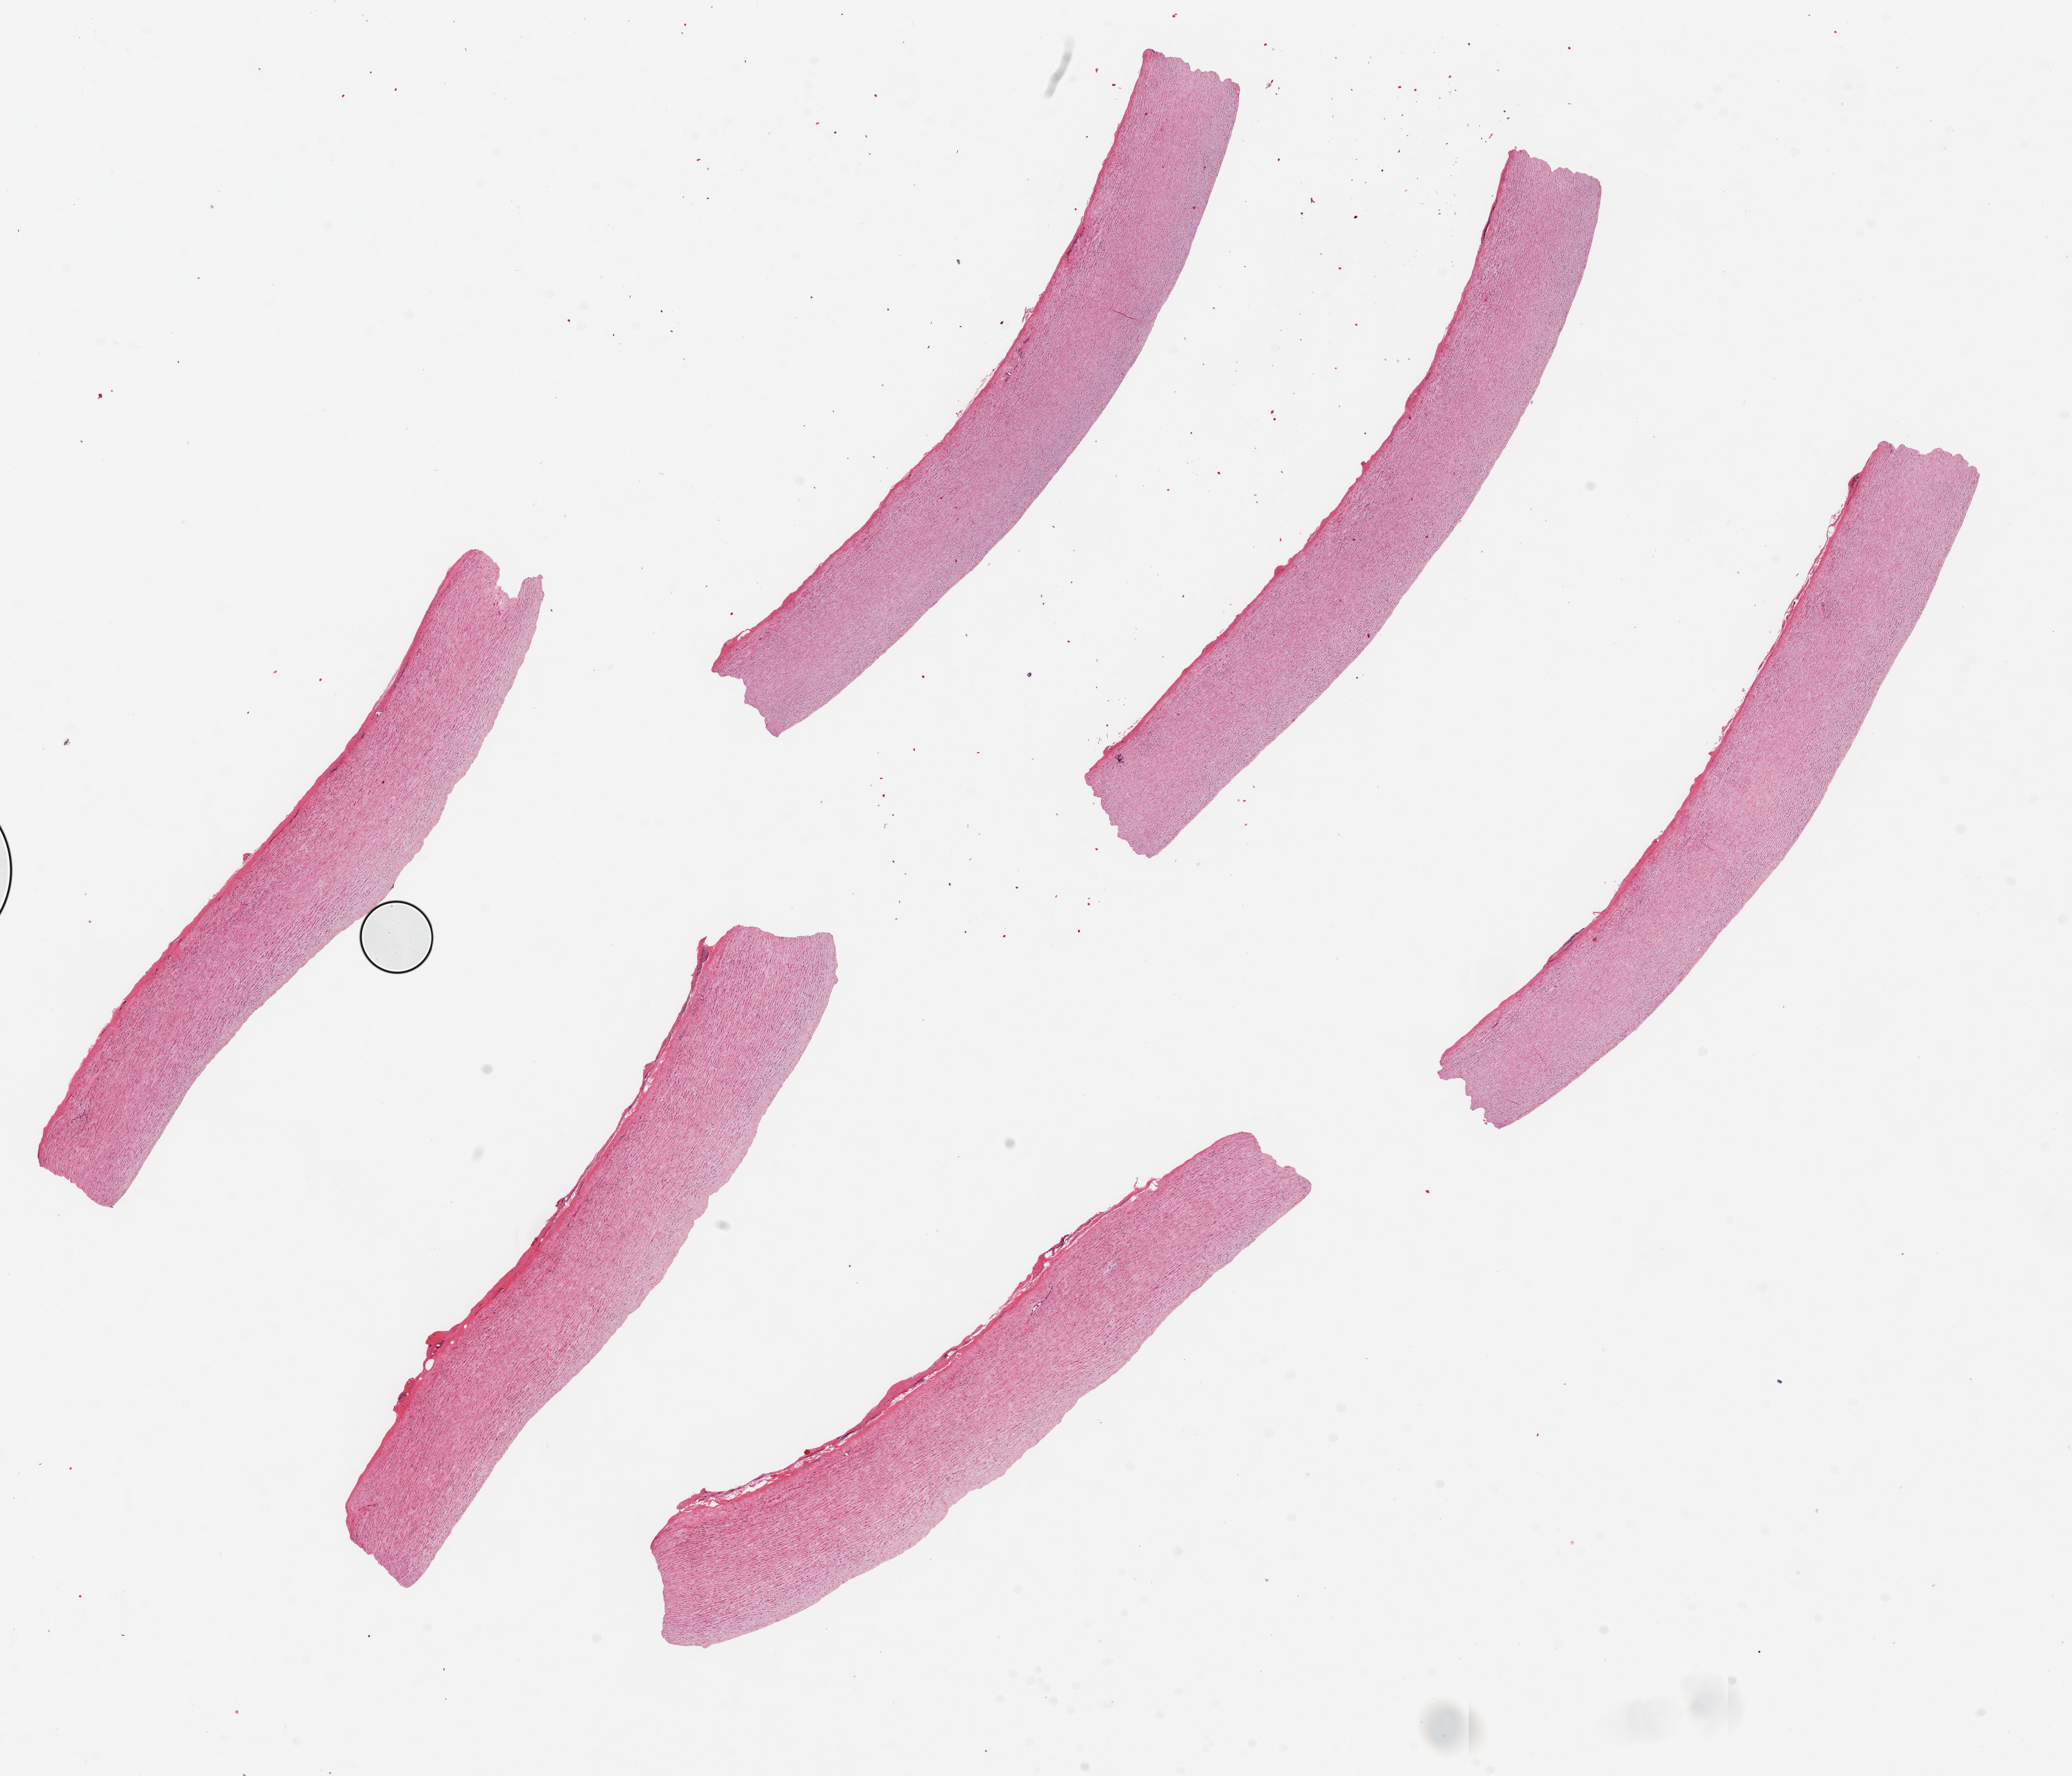
H&E whole-slide image, low-resolution overview of the scanned area, about 23.6 x 20.2 mm (acquisition: 20x scan); PAXgene-fixed, paraffin-embedded tissue; section of aorta (target tissue); tissue donor sample. Donor: female.
• pathologist's review note for this sample: 6 pieces, up to 9x1mm; well trimmed of extraneous stroma